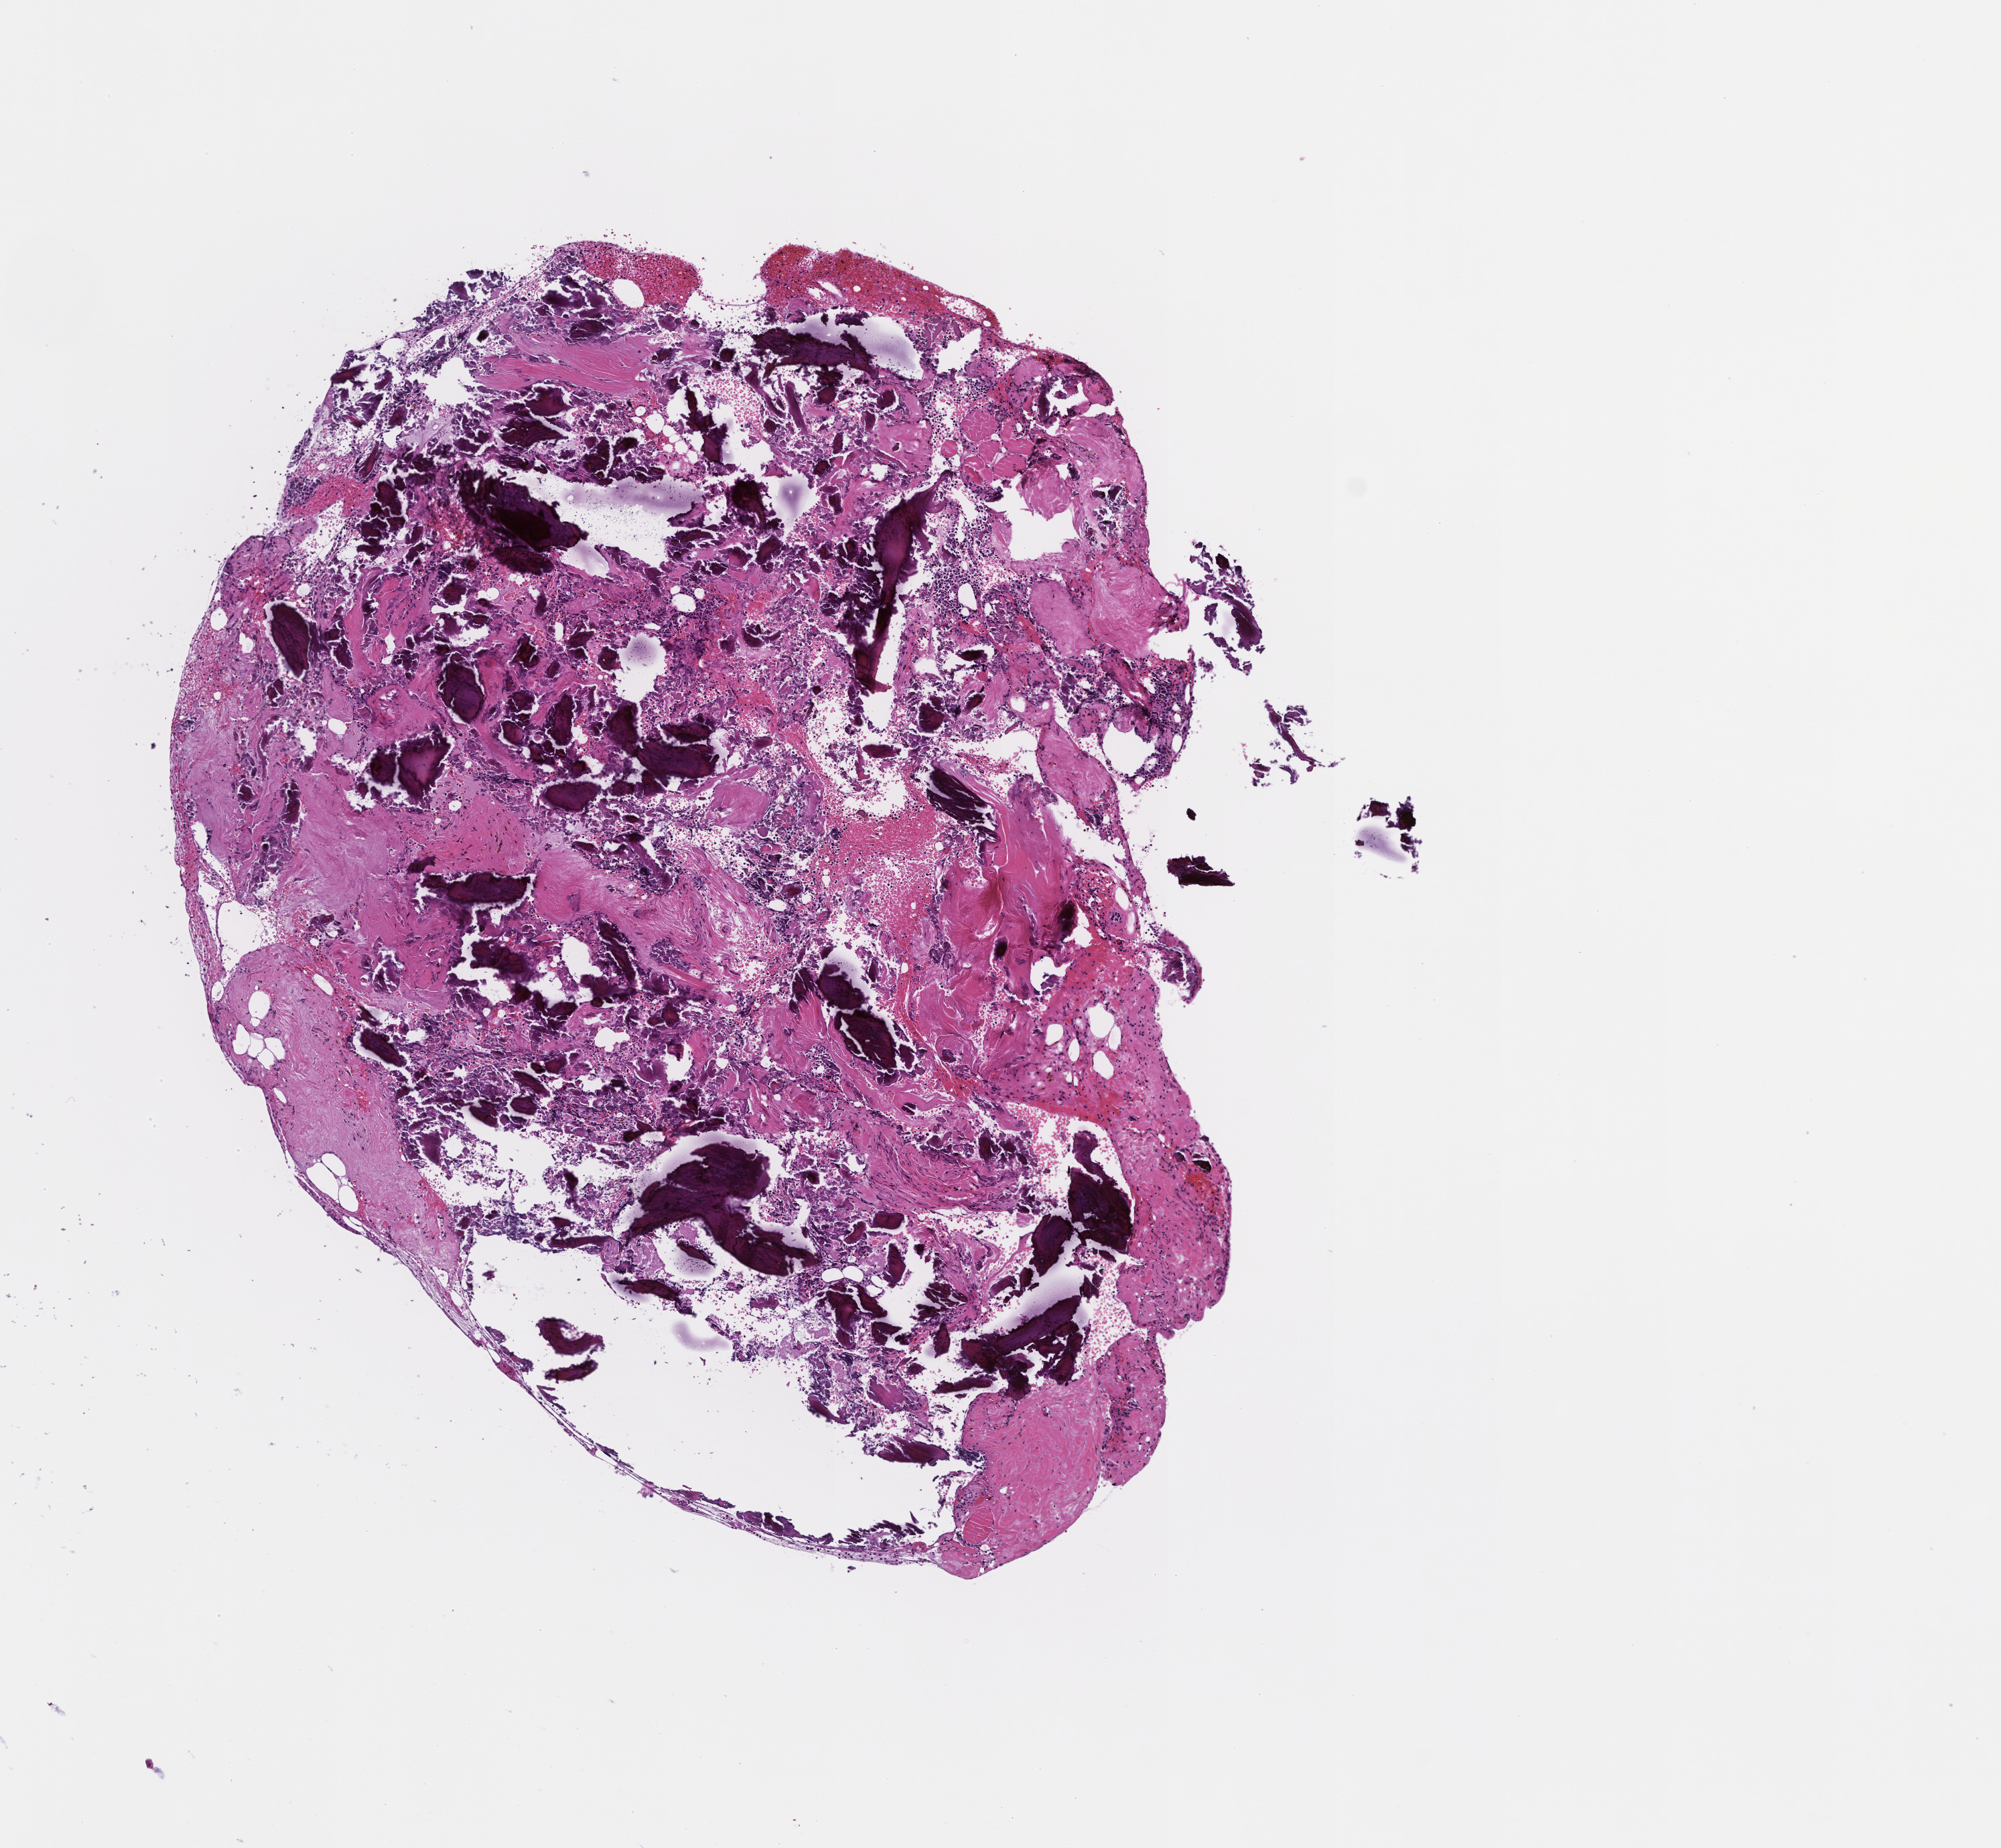
Whole-slide image, H&E stain — a low-resolution overview of the entire scanned area, about 6.0 x 5.6 mm; FFPE section; tissue site: bone marrow; collected on treatment. Female patient.
This section: primary tumor. Diagnosis: Acute Myeloid Leukemia Not Otherwise Specified.